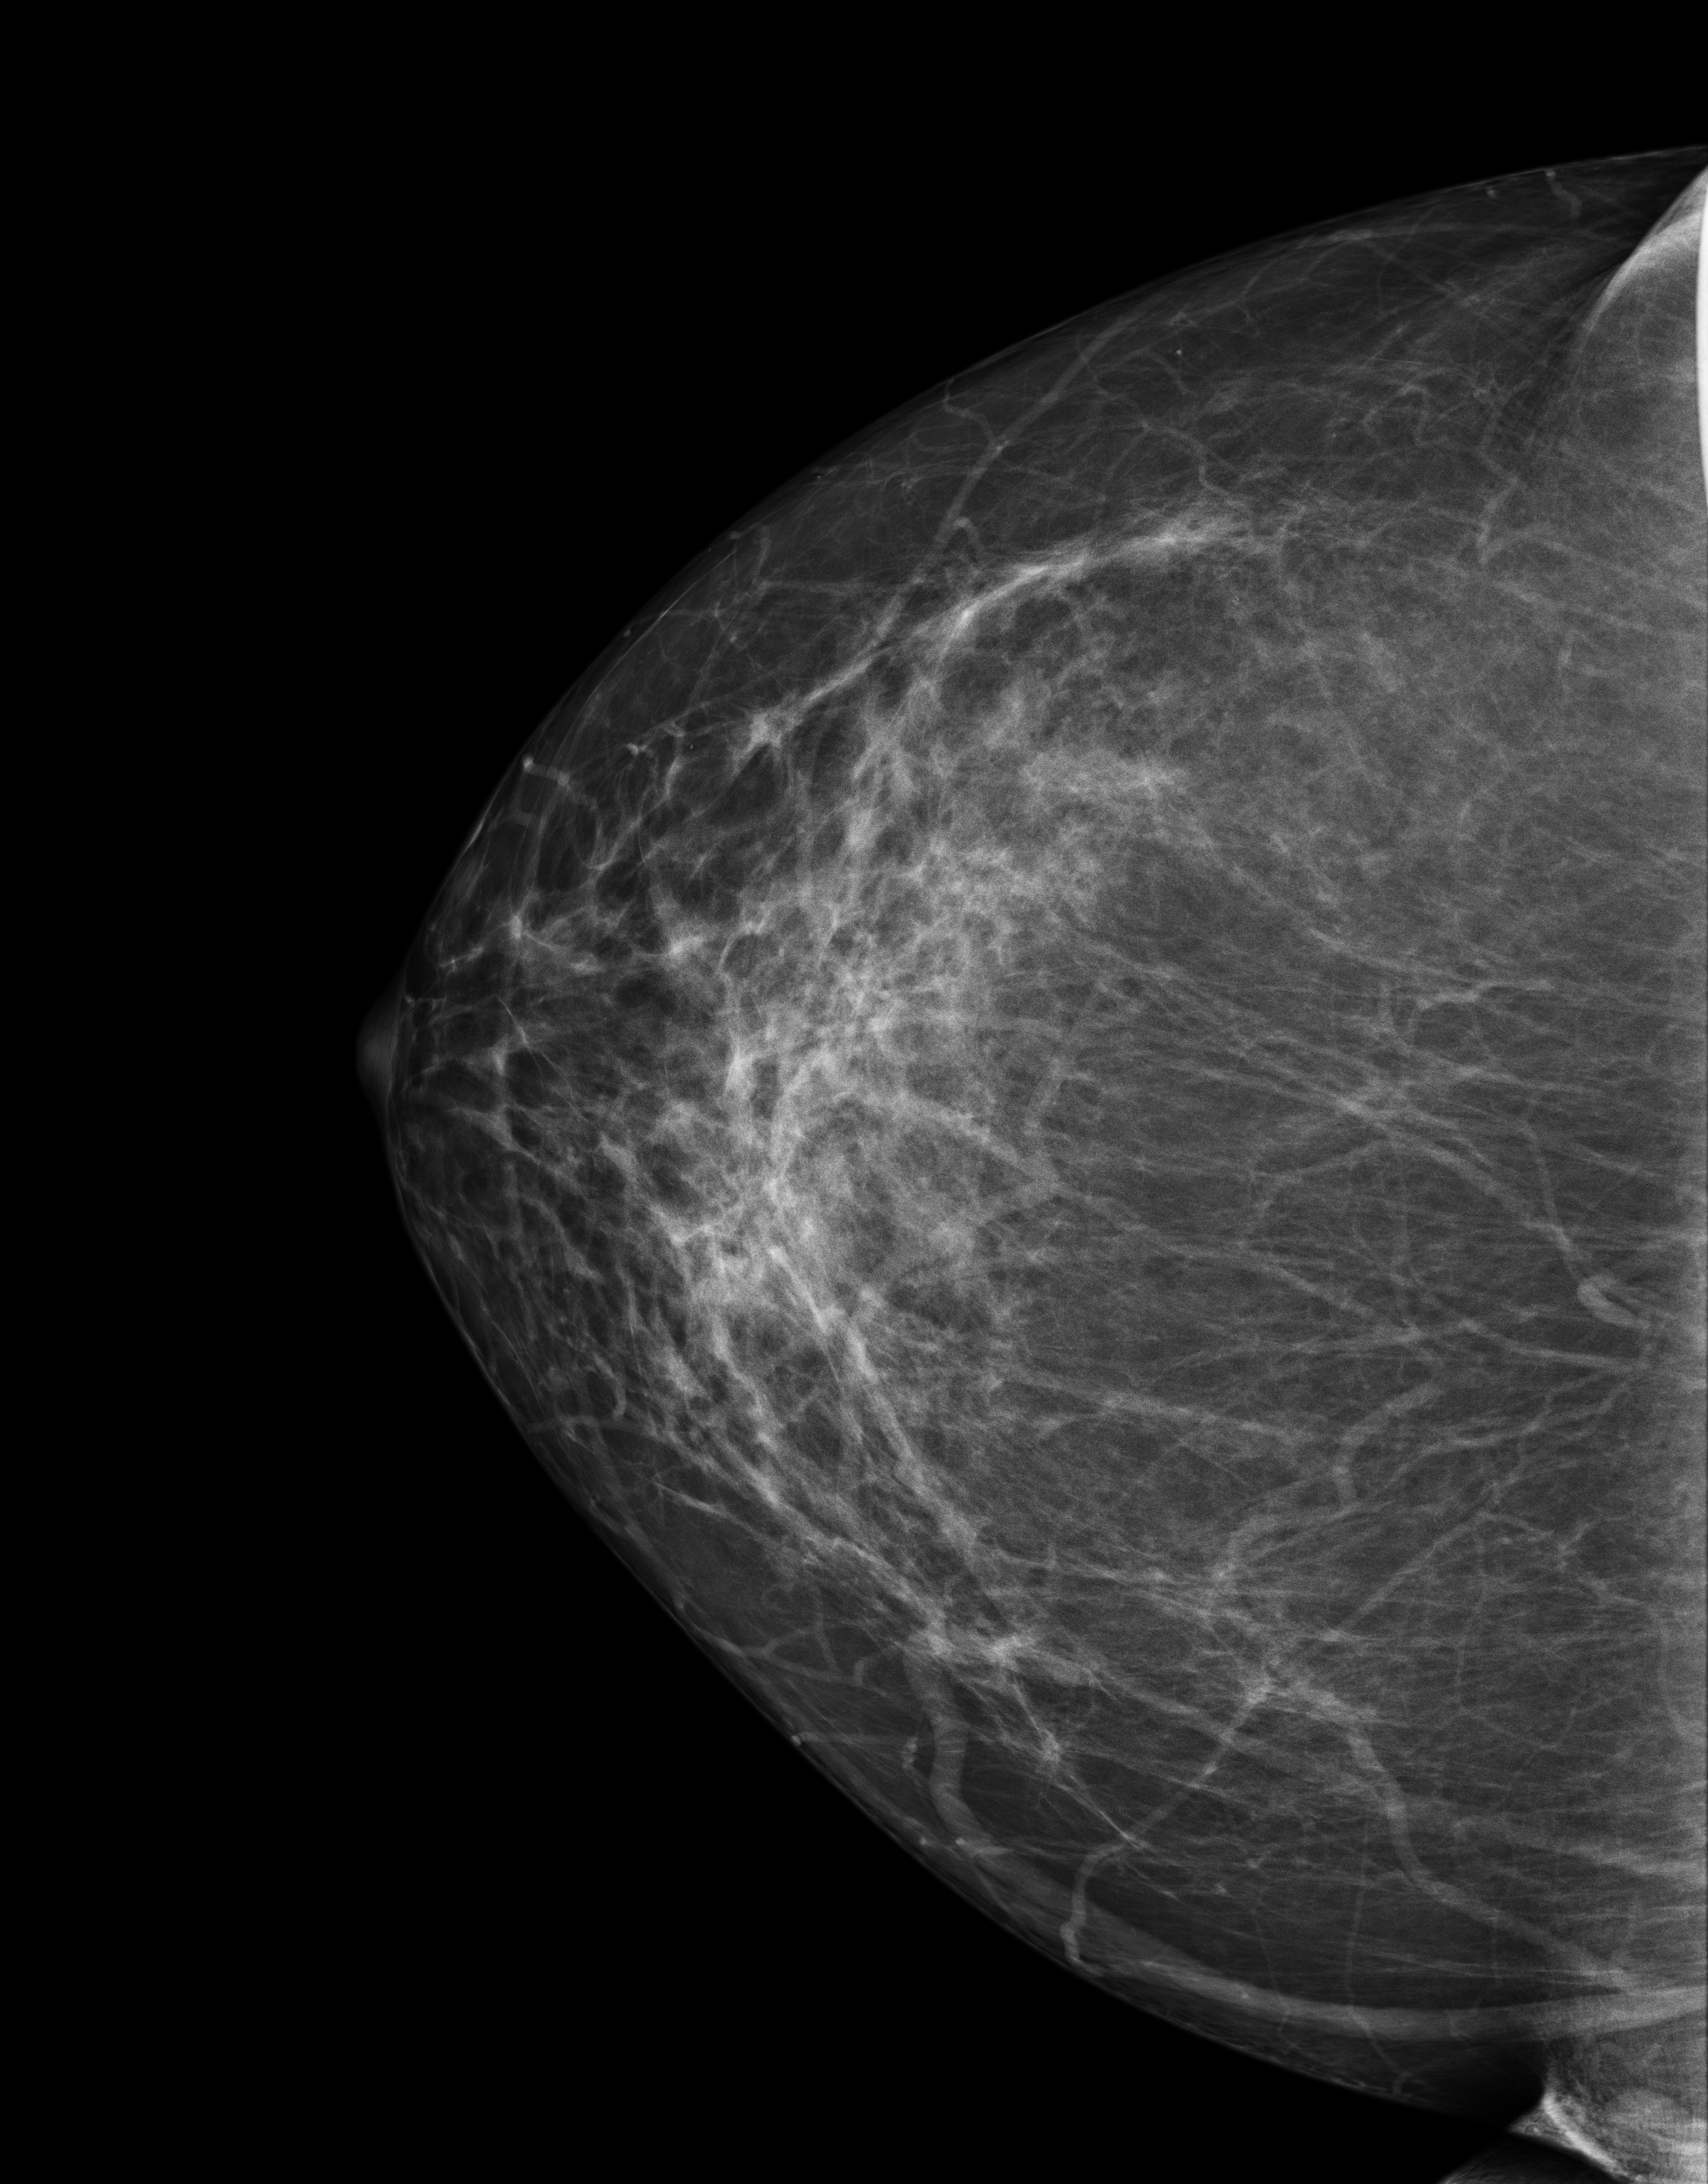
Annual screening mammography examination, system: Senographe Essential ADS_56.21.3. Patient: female, 59 years.
Image type: full-field digital mammogram. Breast: right. Projection: CC view.